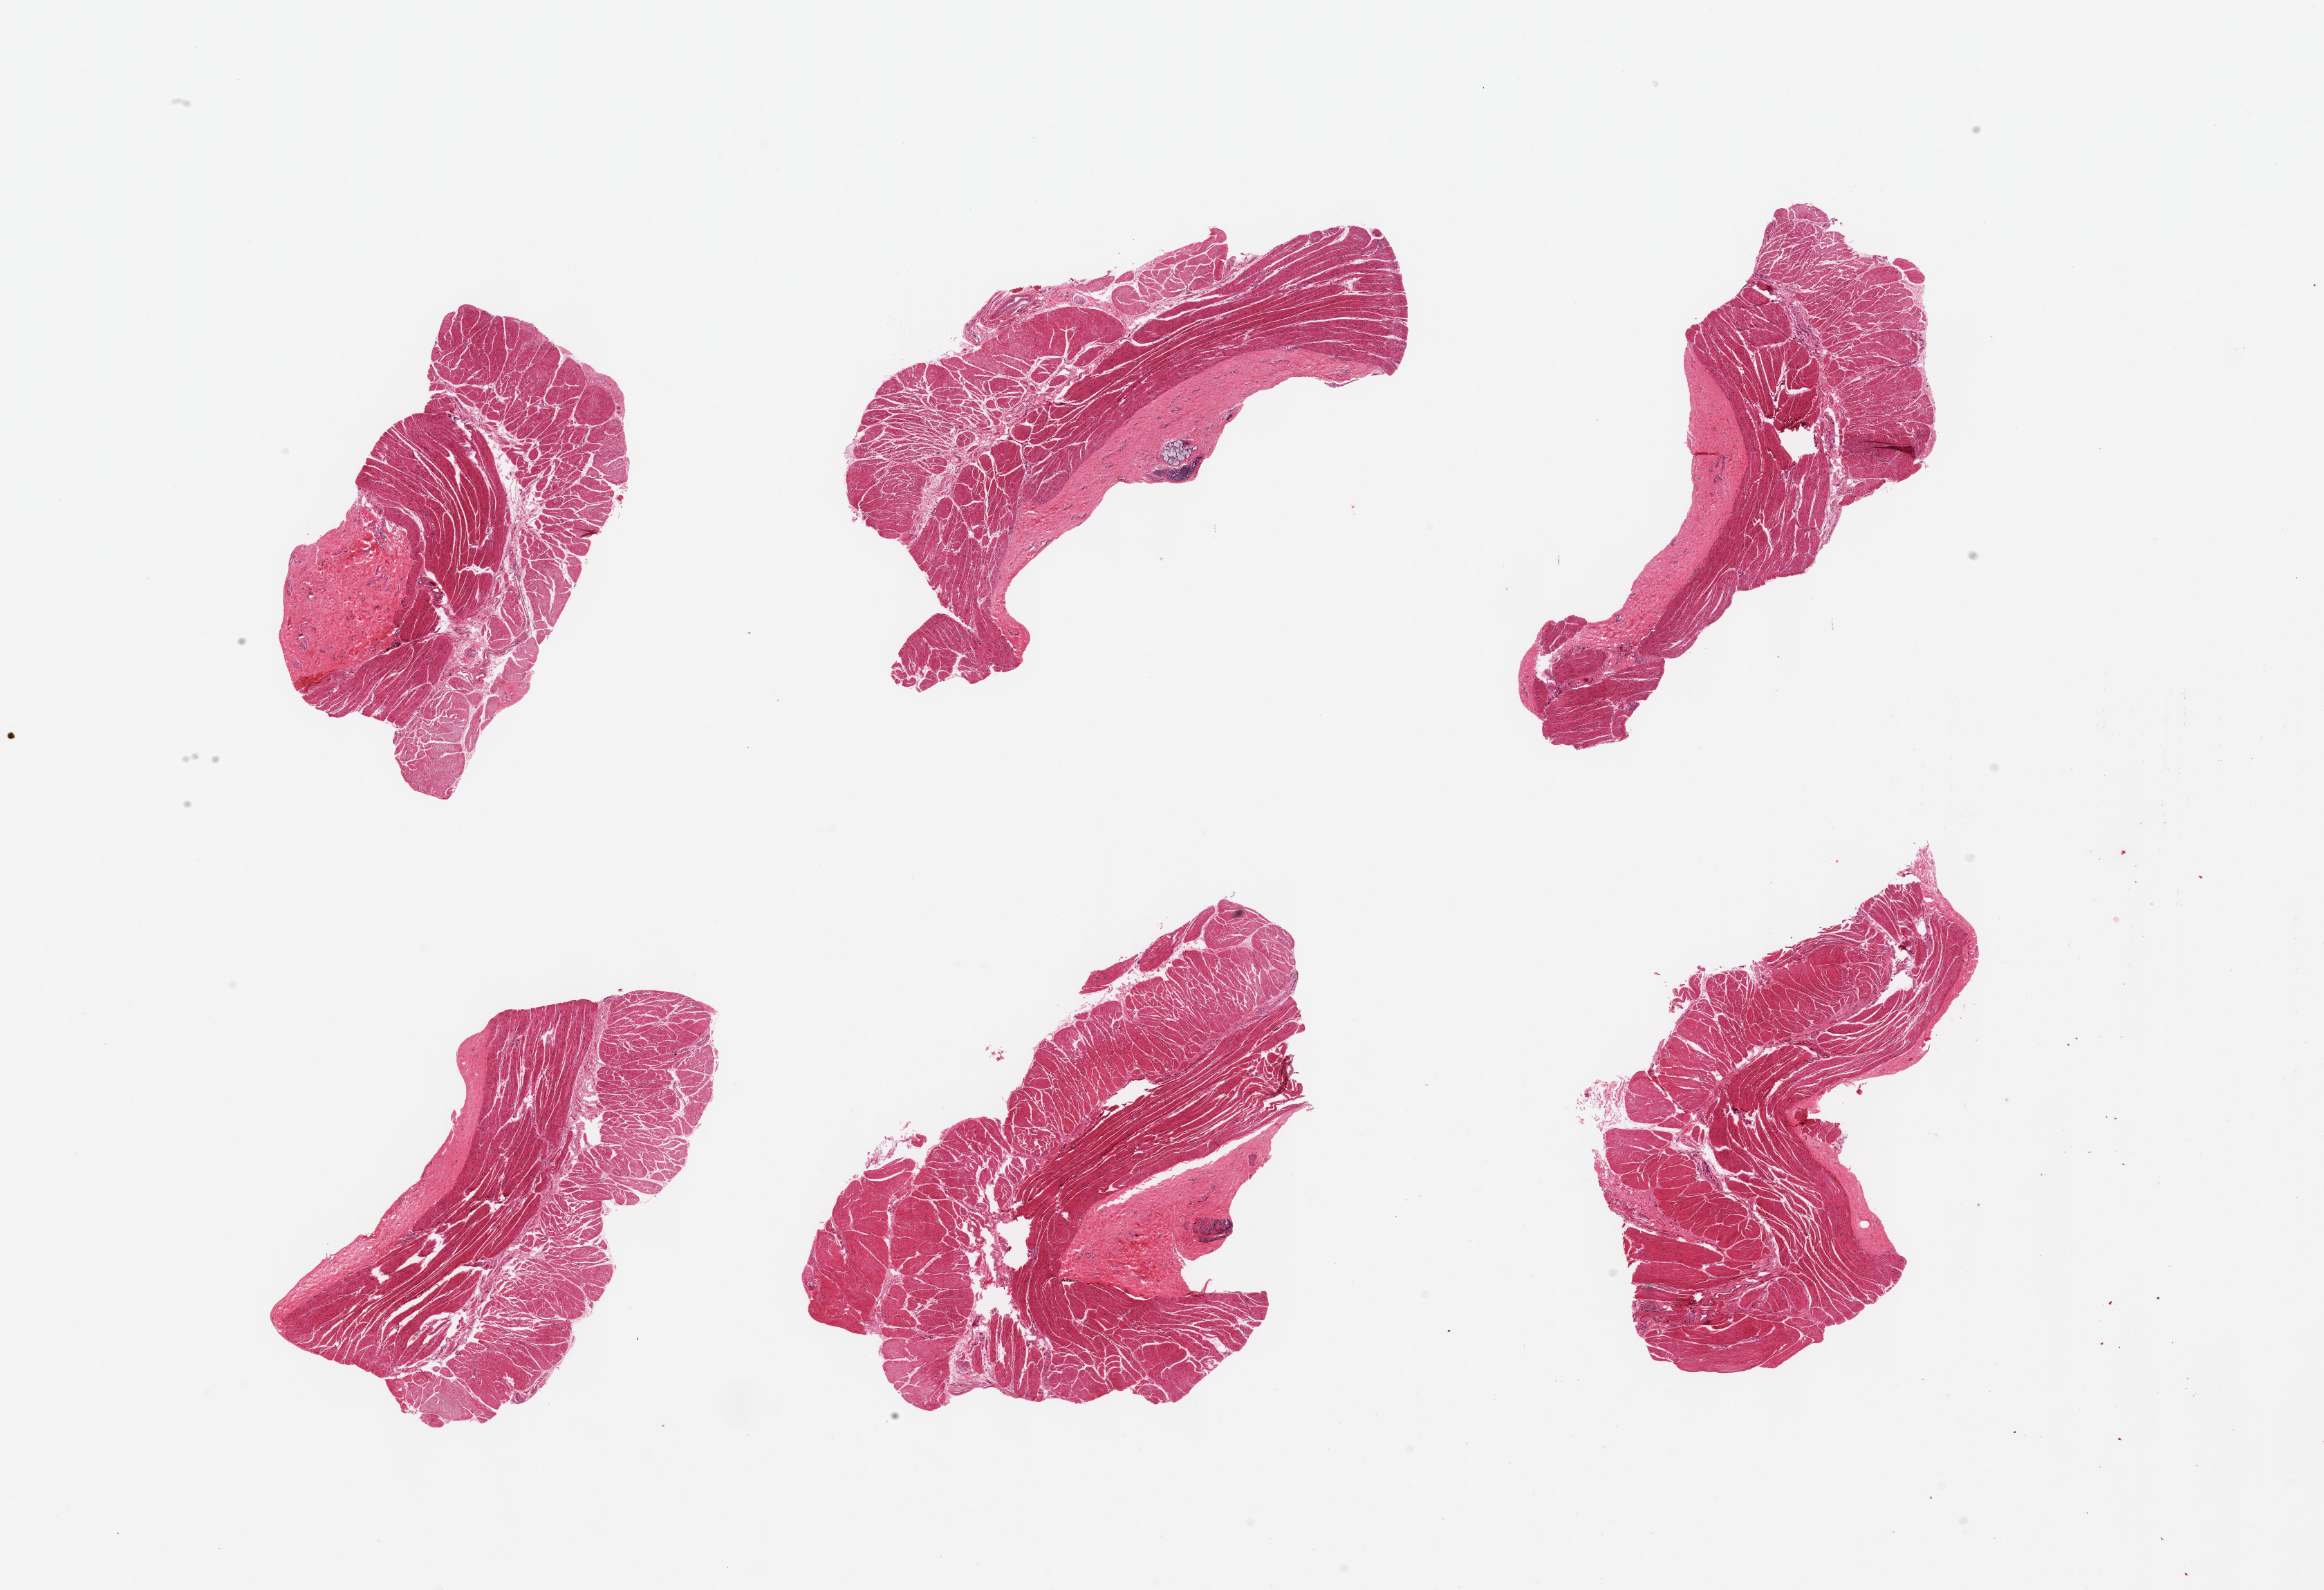
Digitized H&E-stained section, low-resolution overview of the scanned area, about 26.6 x 18.2 mm, PAXgene-fixed paraffin-embedded (PFPE) section, section of esophageal muscle (target tissue), donor tissue sample.
Reviewer comment on this tissue sample: 6 pieces, confirmed target muscularis; incidental mucus gland.